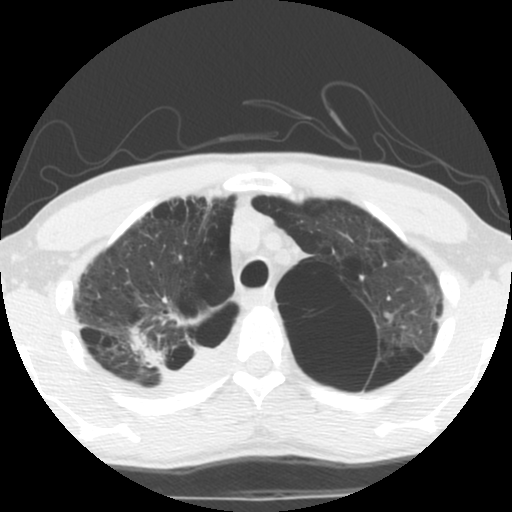
Low-dose screening chest CT, one axial slice; position 93 of 119 along the scan axis; reconstruction kernel STANDARD; lung window (W 1500 / L -600 HU); 2.5 mm slice thickness; 512 × 512 image matrix, field of view 295 × 295 mm.
Annotated regions visible in this slice (expert manual segmentation):
- lesion 1 (tumor, upper lobe of right lung): bounding box (x1, y1, x2, y2) in pixels: (130, 325, 168, 371)